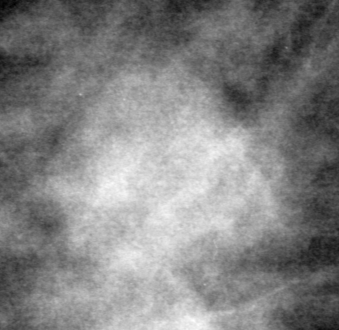
Region of interest cut from a scanned film mammogram (one marked finding), right breast, CC view, BI-RADS breast density category 2 (scale 1–4).
Mass, shape round, margins obscured; BI-RADS assessment category 0; subtlety rating 4 on a 1 (subtle) to 5 (obvious) scale; pathology result (as recorded, not read from the image): benign.